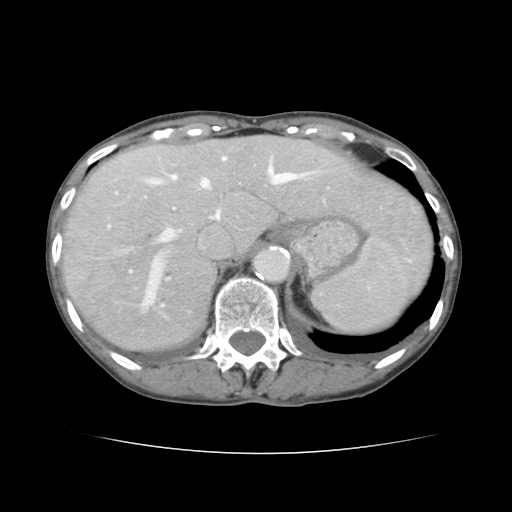
Contrast-enhanced abdominal CT, one axial slice. 120 kVp. Intravenous contrast given. Soft-tissue window (W 400 / L 40 HU). 2.5 mm slice thickness. 512 × 512 image matrix, field of view 319 × 319 mm. Female patient, age 77 years. Case-level facts recorded for this patient, not image findings: diagnosis: colorectal cancer liver metastases, imaged before liver resection; multiple liver metastases: yes; largest metastasis: 3 cm; chemotherapy before resection: yes.
Annotated regions visible in this slice (expert manual segmentation):
- hepatic veins: bounding box (x1, y1, x2, y2) in pixels: (108, 157, 307, 308)
- liver: (61, 136, 432, 352)
- planned liver remnant (the part of the liver to remain after resection): (164, 136, 432, 276)
- portal vein (with intrahepatic branches): (108, 174, 383, 228)